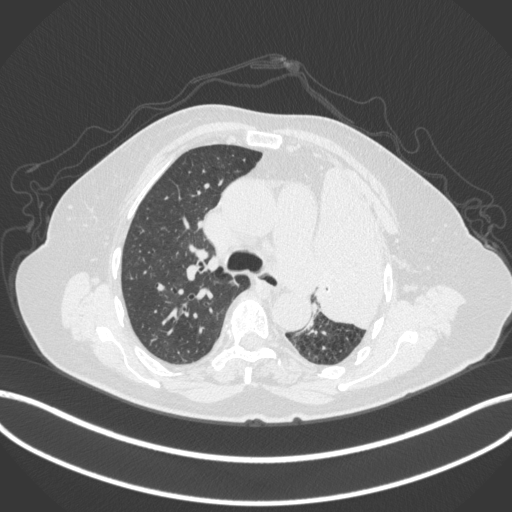
Chest CT, one axial slice. Position 259 of 399 along the scan axis. Reconstruction kernel B31f. 120 kVp. Lung window (W 1500 / L -600 HU). 1 mm slice thickness. 512 × 512 image matrix. Female patient, age 75 years. From the clinical record (not read from this slice): clinical TNM (as recorded): T3 N3 M1.
Annotated regions visible in this slice (rectangle marked by the reading radiologist):
- lung tumour (recorded histology: adenocarcinoma): bounding box [x1, y1, x2, y2] px = [312, 158, 398, 339]